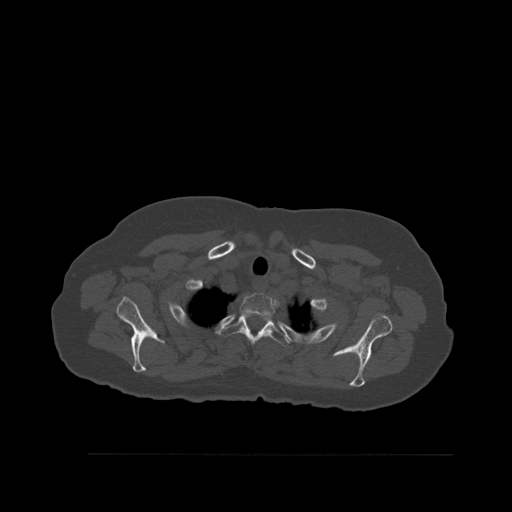
CT including the spine, one axial slice. Slice 436 of 527 in the series (ordered by position). Bone window (W 1800 / L 400 HU). 512 × 512 image matrix, field of view 470 × 470 mm. Female patient, age 73 years. Case-level facts recorded for this patient, not image findings: primary cancer: breast; vertebrae with lytic lesions (as recorded): L2.
Annotated regions visible in this slice (semi-automatically segmented with operator editing):
- T1 vertebra: bounding box (x1, y1, x2, y2) in pixels: (240, 292, 276, 329)
- T2 vertebra: (218, 312, 292, 347)